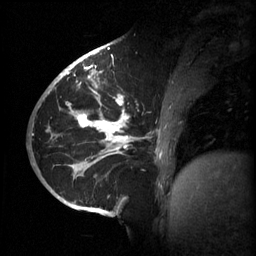
Breast MRI (dynamic contrast-enhanced), one sagittal slice. Slice 24 of 60 in the series (ordered by position). 3 images stored at this slice position (order not interpretable as contrast timing). 1.5 T. TE 4.2 ms, TR 11 ms. 256 × 256 image matrix, field of view 220 × 220 mm. Patient: female, 51 years.
Structures marked on this image (semi-automatic segmentation, software-assisted and operator-edited):
- analysis volume of interest (the breast-tissue region the enhancement analysis was run in; not a lesion): box from (x=63, y=80) to (x=187, y=201) px
- tumour enhancement mask (voxels above the 70 % enhancement threshold inside the analysis volume of interest): (x=66, y=80)–(x=163, y=197)